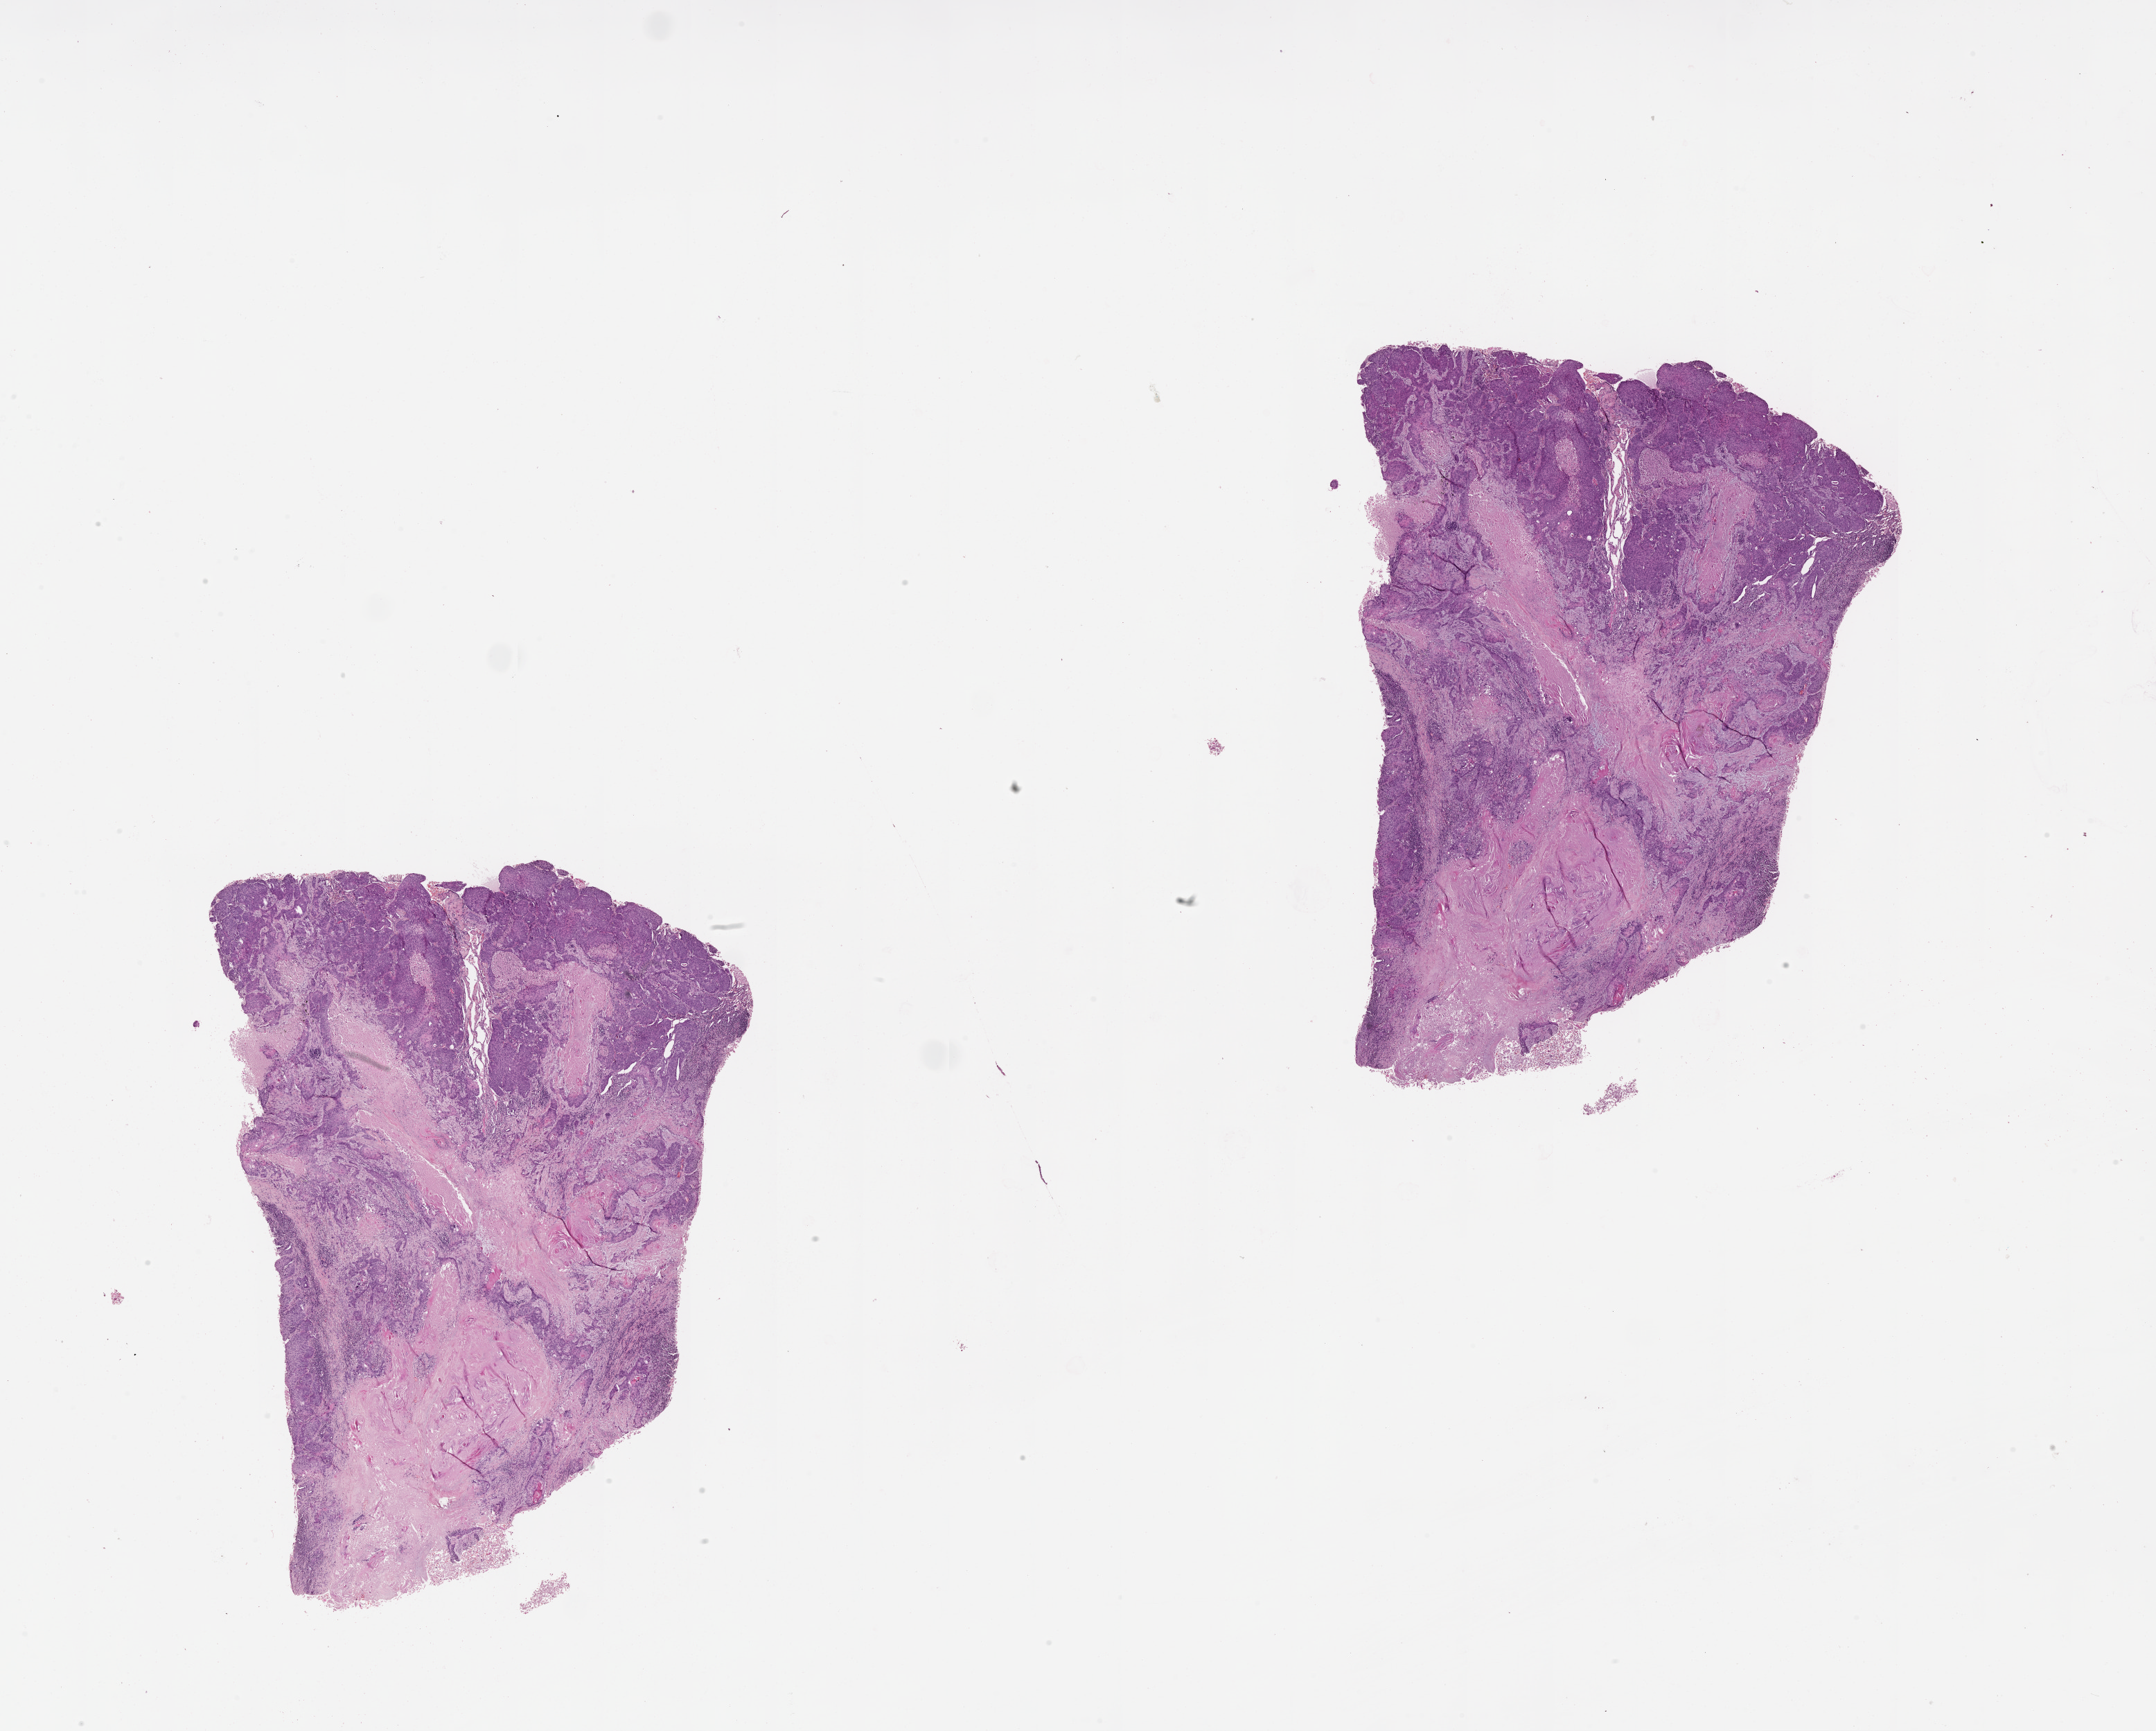
Digitized H&E-stained tissue section (whole slide), shown as a low-resolution overview of the whole scanned area (about 25.1 x 20.1 mm, acquisition: 20x scan); lung, tumour tissue. 60-year-old female patient.
Patient diagnosis (cohort enrolment): squamous cell carcinoma (lung).